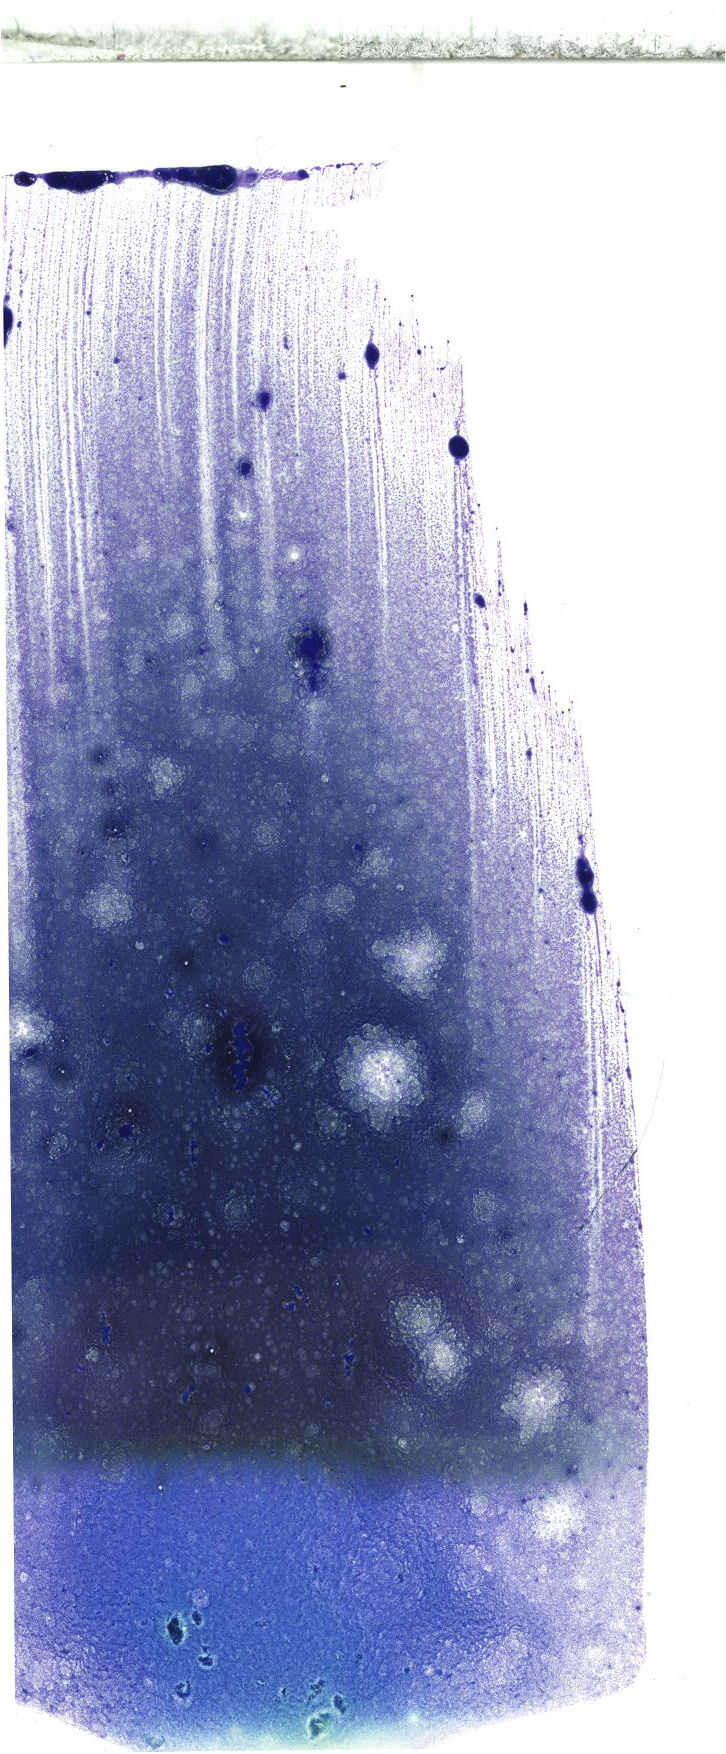
May-Grünwald–Giemsa-stained marrow aspirate smear (whole slide), whole scanned area (about 20.6 x 49.7 mm) shown as a low-resolution overview. Patient sex: male.
Diagnosis: Chronic Phase Chronic Myeloid Leukemia, BCR-ABL1 Positive.